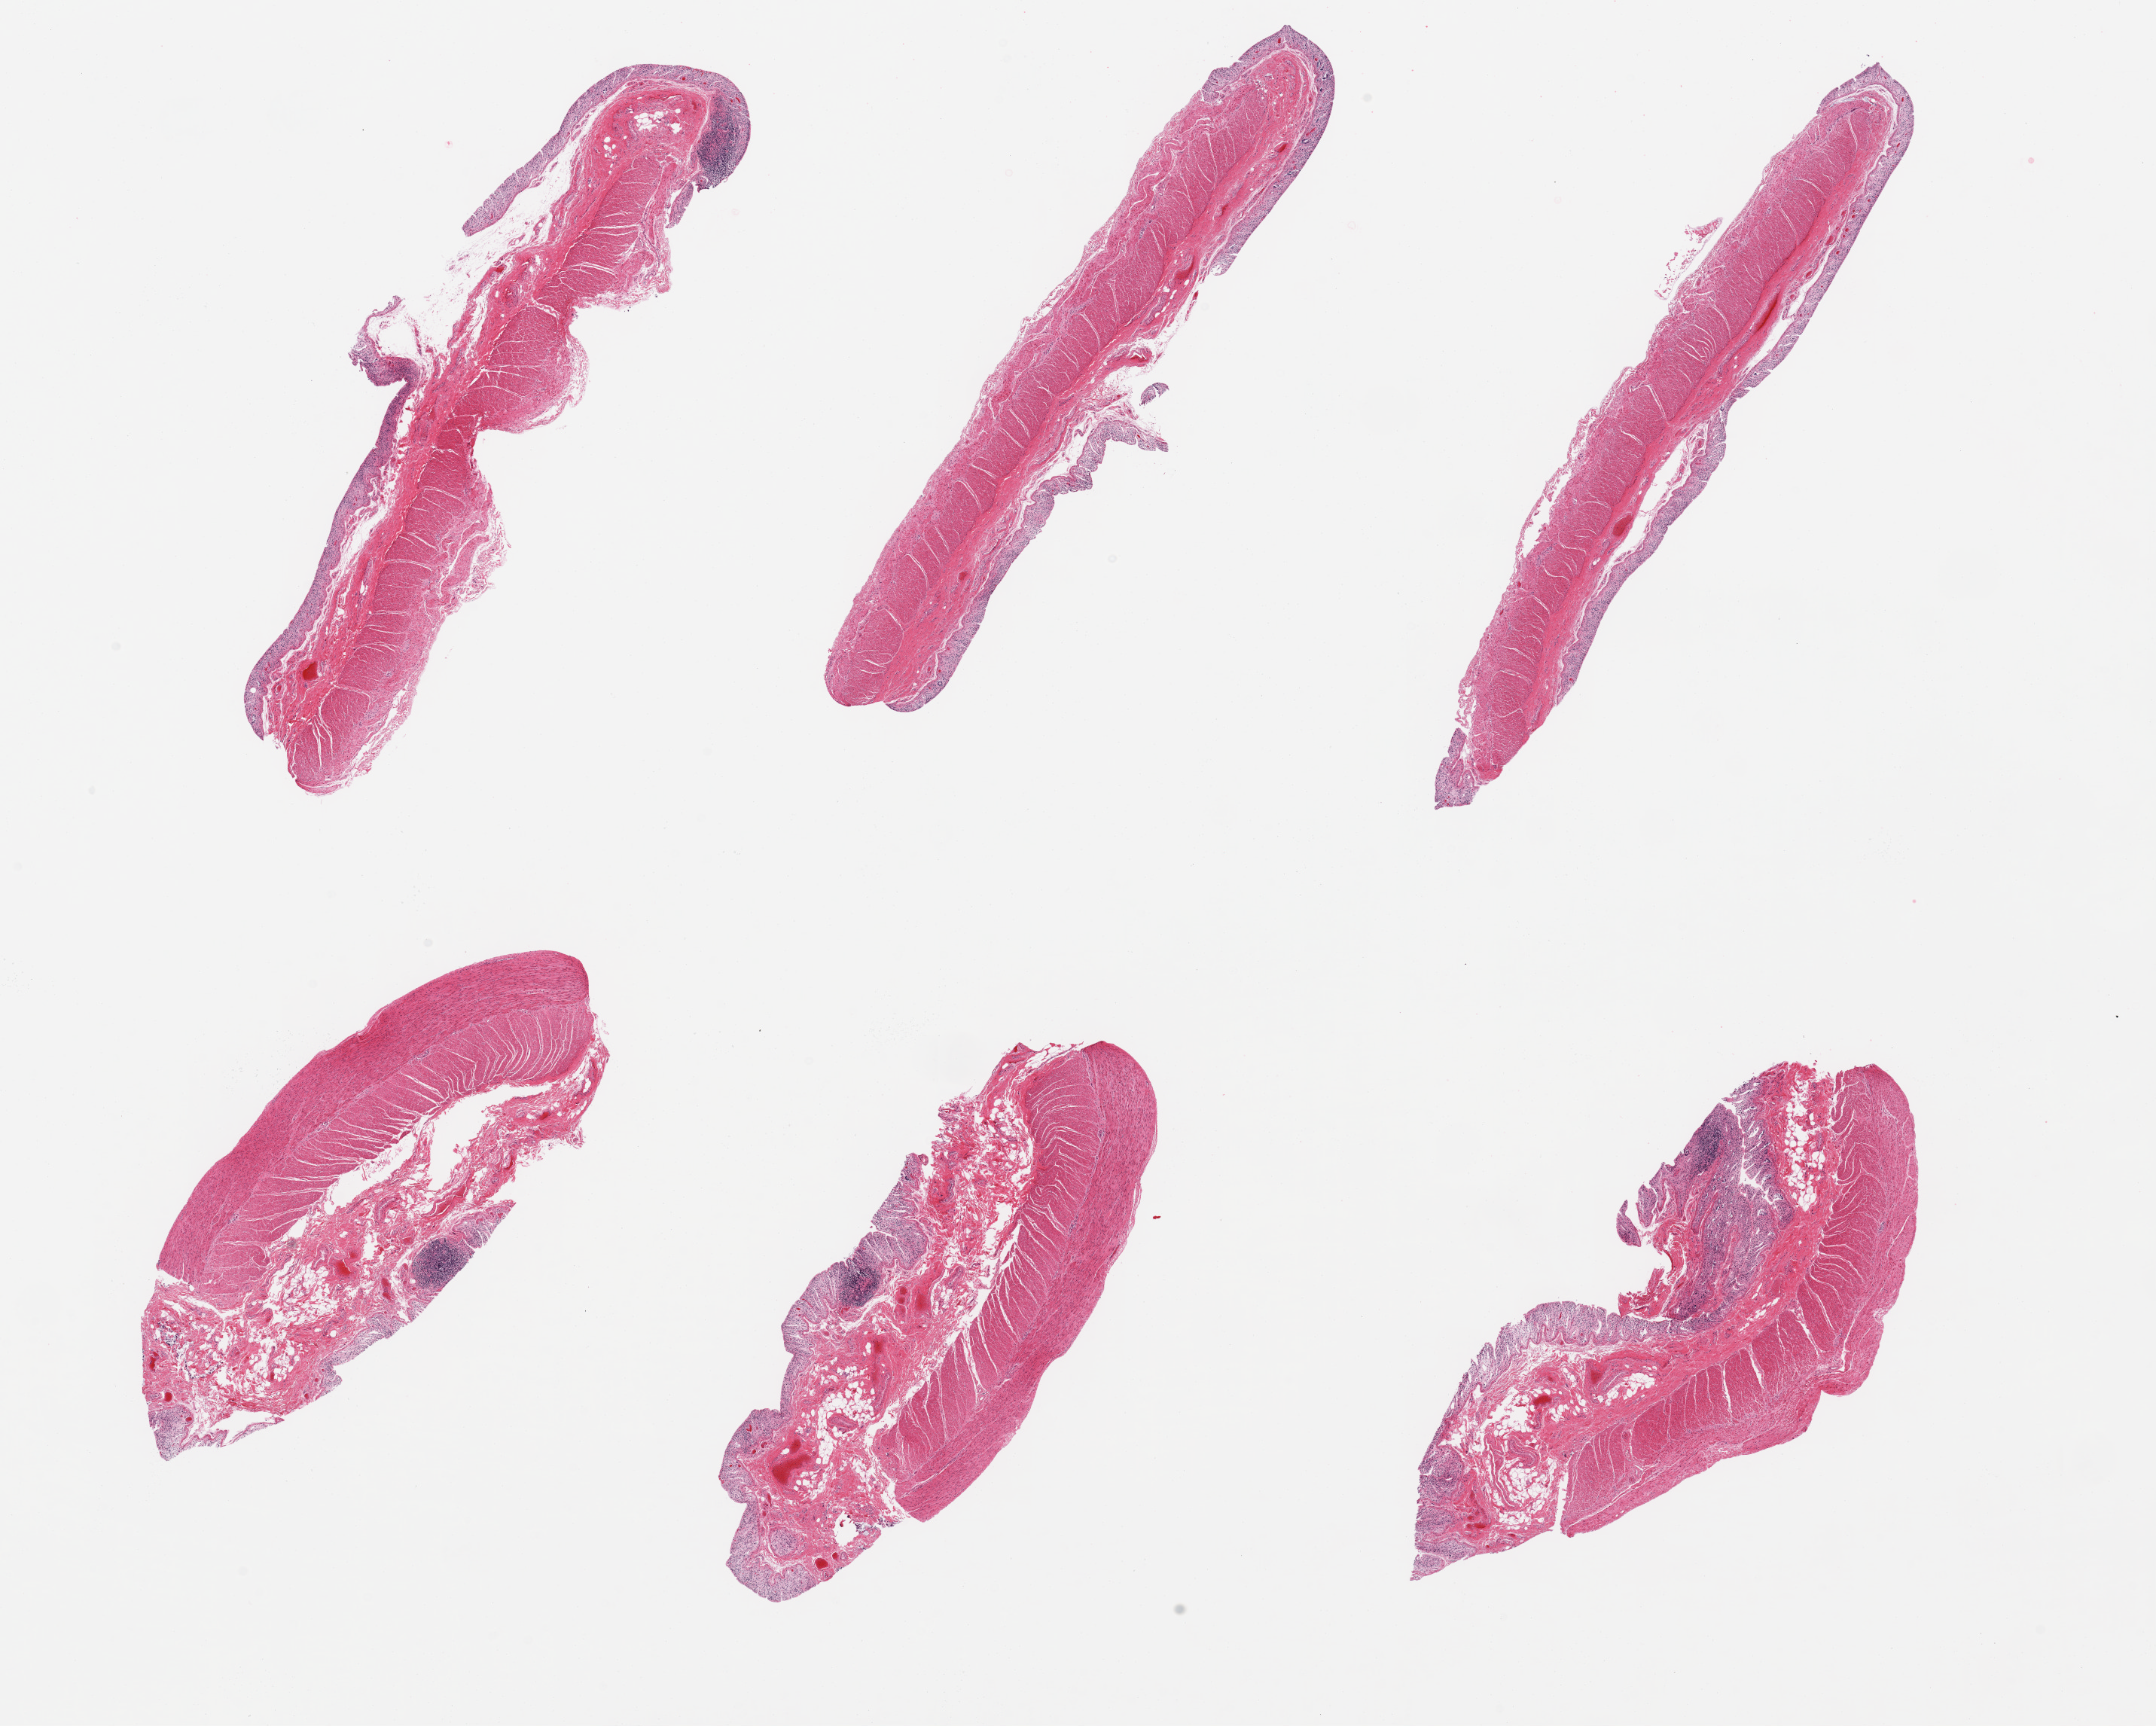
Digitized H&E-stained section, brightfield — low-resolution overview of the scanned area, about 22.6 x 18.1 mm; PAXgene-fixed, paraffin-embedded tissue; section of transverse colon (target tissue); donor tissue sample. Male donor.
Pathologist's review note for this sample: 6 pieces; mucossa completely autolyzed; muscle intact, but with patchy fibrosis.